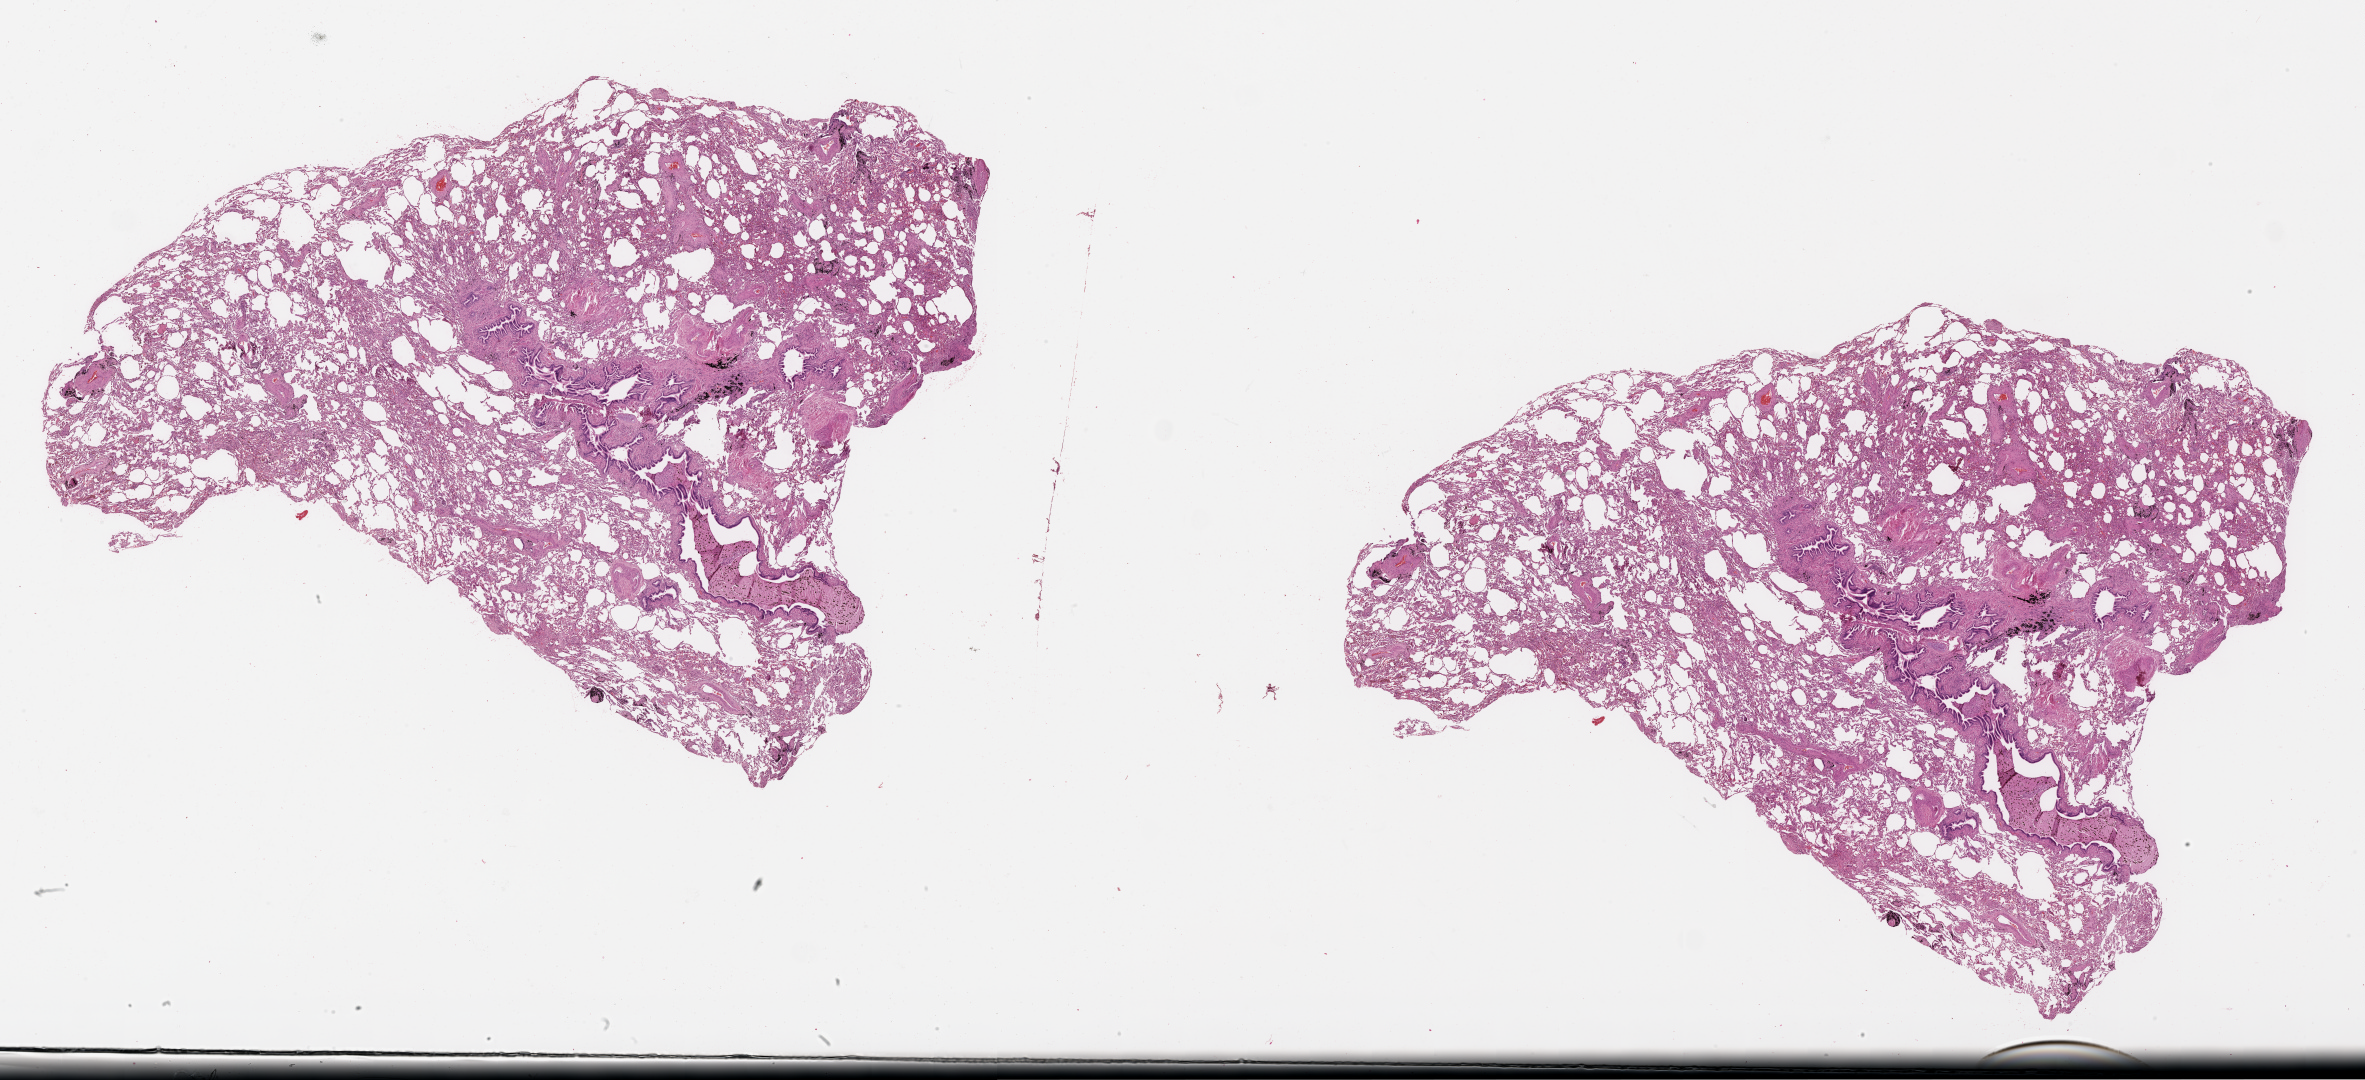
Digitized H&E tissue section (whole slide) — a low-resolution overview of the entire scanned area, about 38.1 x 17.4 mm (acquisition: 20x scan), lung, normal (non-tumour) tissue. 77-year-old male patient.
This section: normal (non-tumour) tissue from the same patient. Patient diagnosis (cohort enrolment): squamous cell carcinoma (lung).